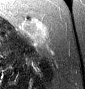
MRI of an extremity soft-tissue mass, one axial slice. Slice 28 of 46 in the series (ordered by position). T2-weighted fat-saturated. MR volume resampled by the dataset authors to the PET/CT grid (not the native acquisition matrix). 3.27 mm slice thickness. 85 × 89 image matrix. Female patient. From the clinical record (not read from this slice): histological type: leiomyosarcoma; grade: intermediate; site of the primary tumour: parascapusular.
Structures marked on this image (expert contour drawn on MRI and transferred to this co-registered scan by the dataset authors):
- gross tumour volume including surrounding oedema: bounding box [x1, y1, x2, y2] px = [20, 19, 48, 45]
- gross tumour volume (mass): [22, 19, 42, 38]